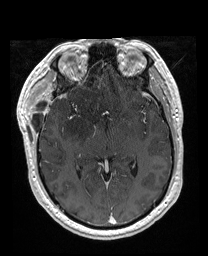
Brain MRI from a brain-tumour surgery series, one axial slice; position 103 of 176 along the scan axis; T1-weighted post-contrast; 1 mm slice thickness; 208 × 256 image matrix, field of view 208 × 256 mm. Case-level facts recorded for this patient, not image findings: histopathology: Astrocytoma; WHO grade: 4; IDH mutation: yes.
Outlined on this slice (expert manual segmentation):
- previous resection cavity: box from (x=73, y=56) to (x=91, y=81) px